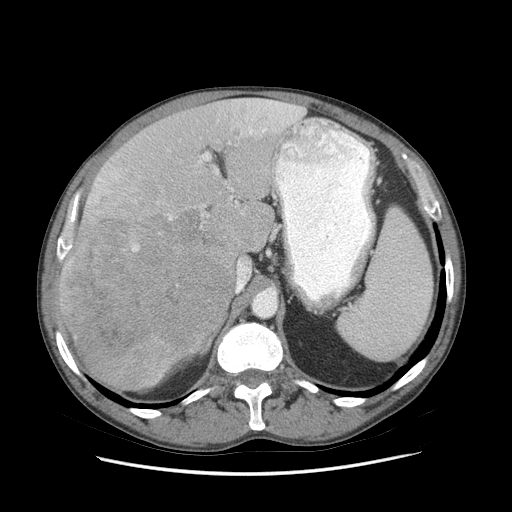
Contrast-enhanced abdominal CT (liver protocol), one axial slice. Position 51 of 89 along the scan axis. Reconstruction kernel STANDARD. 140 kVp. Soft-tissue window (W 400 / L 40 HU). 2.5 mm slice thickness. 512 × 512 image matrix, field of view 380 × 380 mm. Case-level facts recorded for this patient, not image findings: diagnosis: hepatocellular carcinoma (patient treated with transarterial chemoembolisation; whether this scan precedes or follows treatment is not stated here); TNM stage (as recorded): Stage-IIIB; Child-Pugh class: A; tumour nodularity: multinodular.
Annotated regions visible in this slice (semi-automatic segmentation, software-assisted and operator-edited):
- liver parenchyma outside the tumour (the mass and vessels are separate outlines, so this box may not span the whole liver): bounding box <56,98,304,390> (left, top, right, bottom; pixels)
- mass: <59,209,236,389>
- liver vessels: <61,100,301,259>